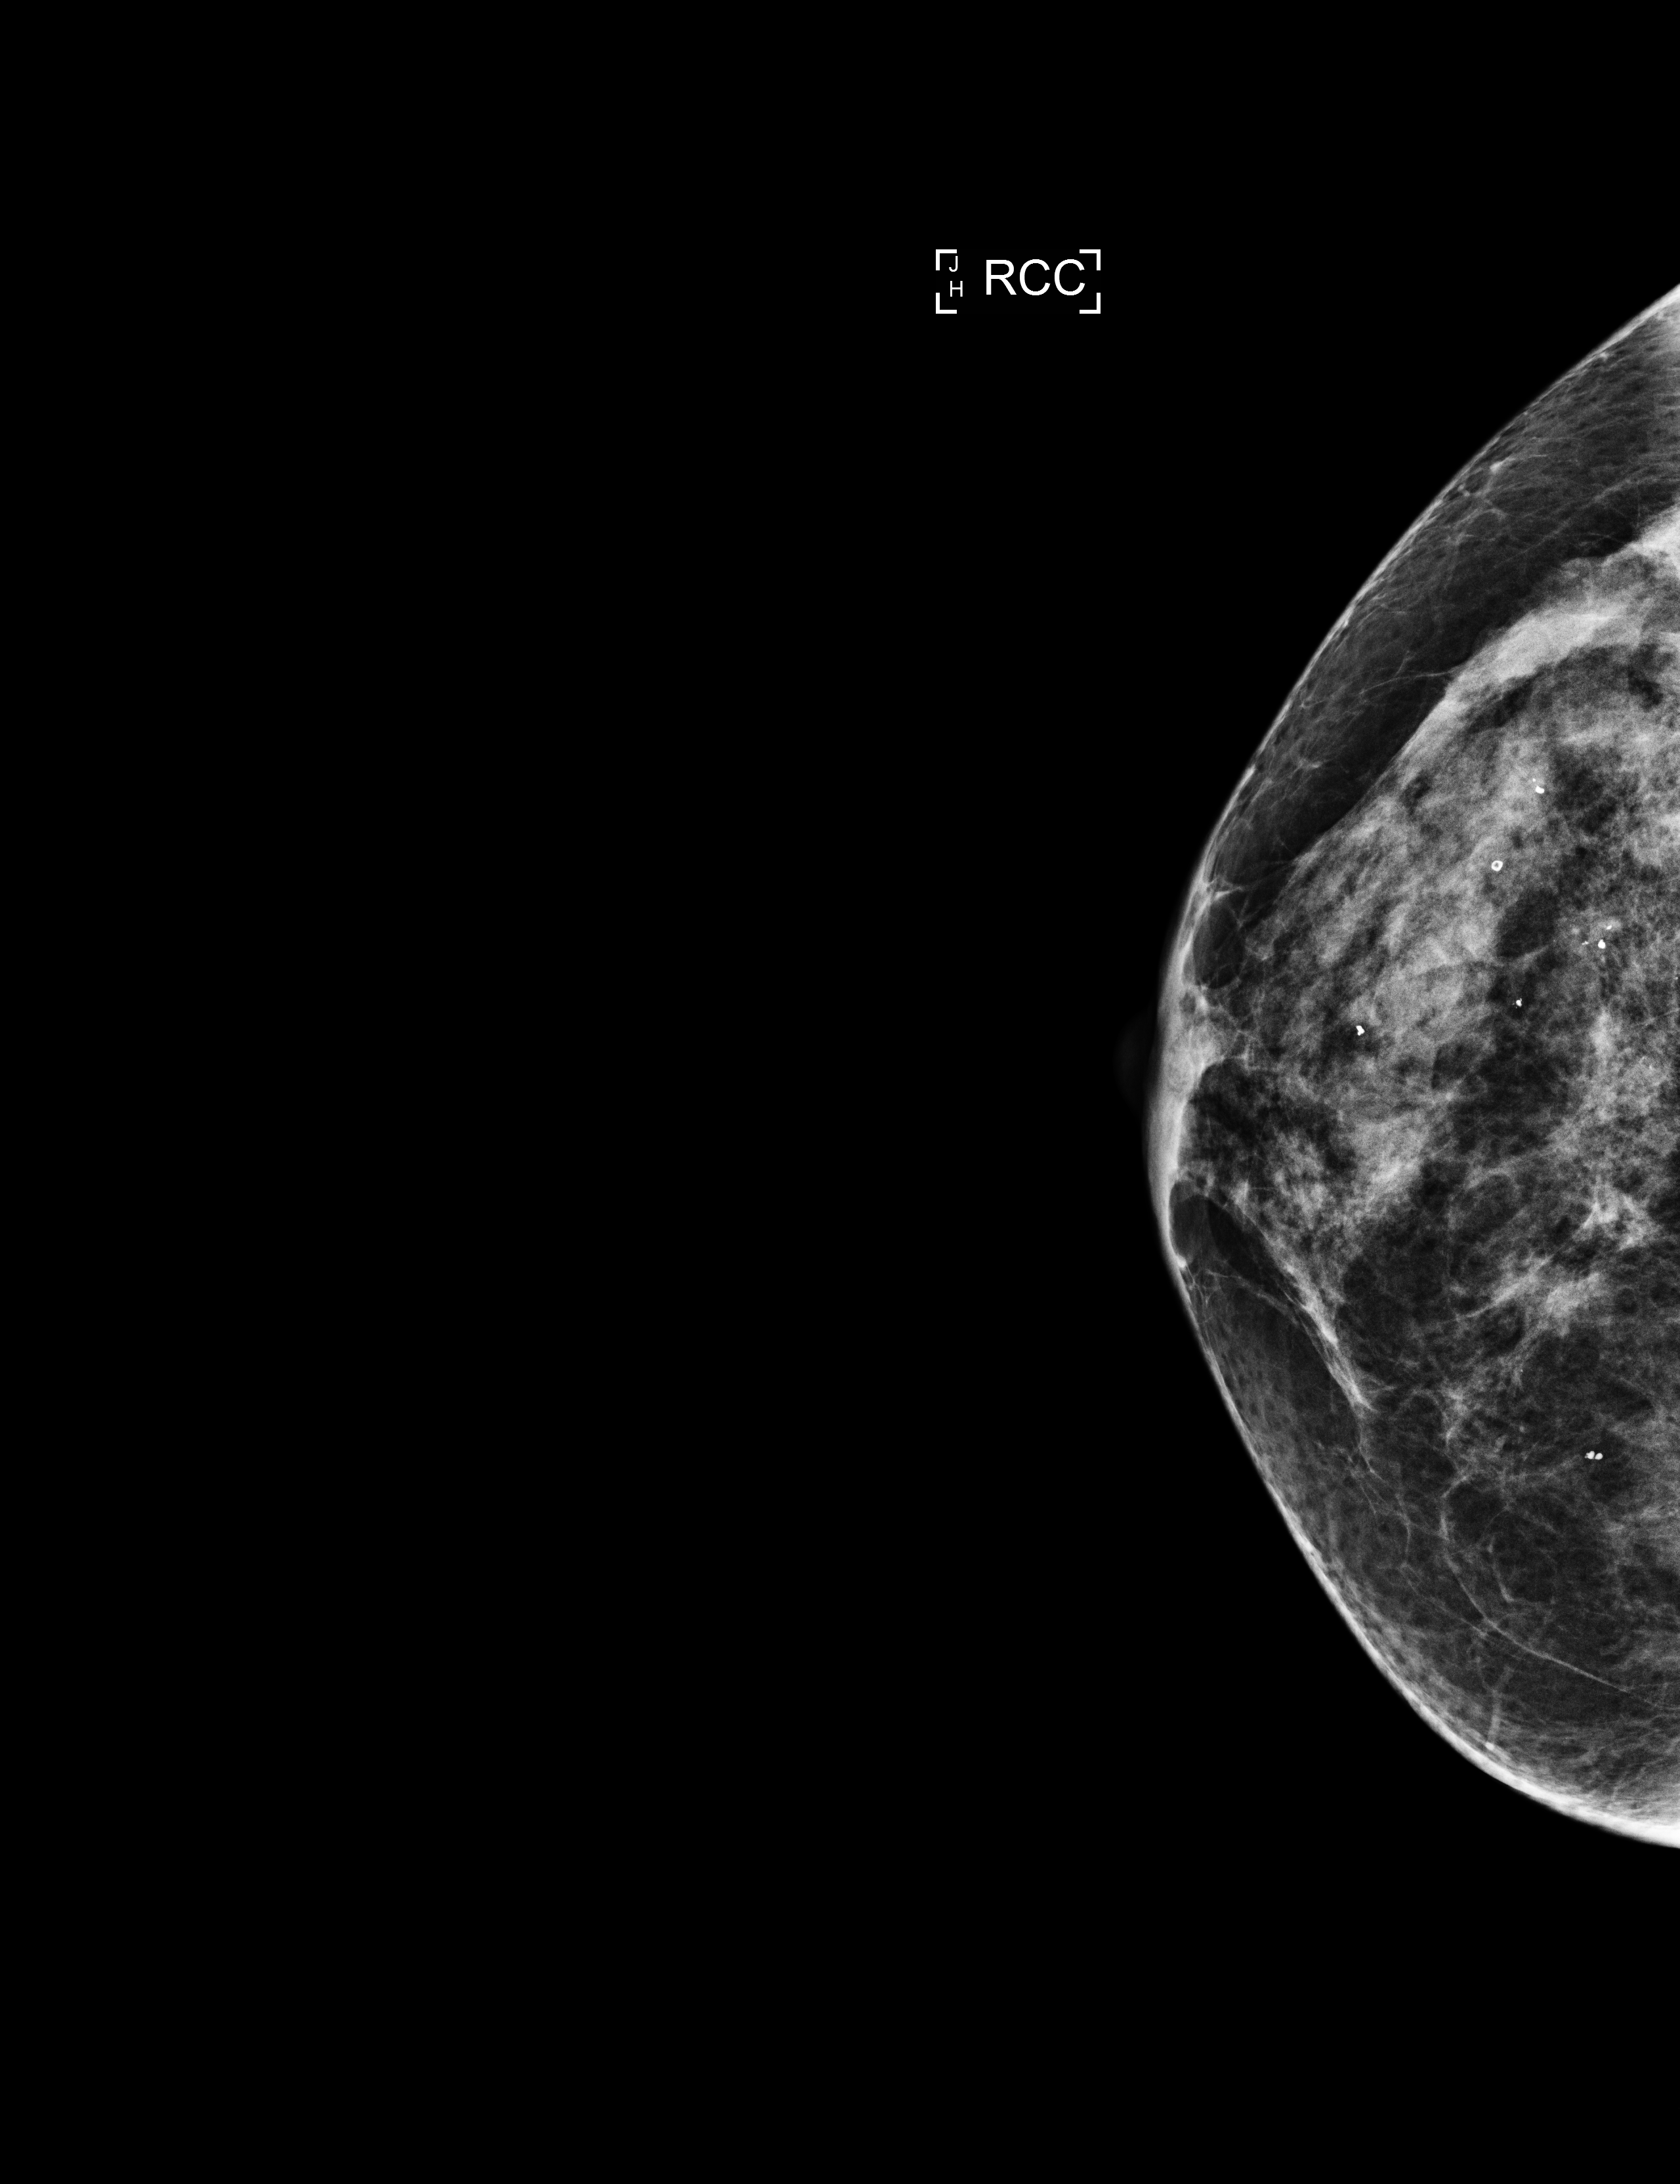
Digital mammogram (FFDM); right breast; CC view; screening examination. Female patient, age 74 years.
- BI-RADS breast density category at the screening exam (both breasts, scale 1–4): 3
- final BI-RADS category for the screening round (tomosynthesis exam, both breasts): category 2
- recall: no recall after this screen